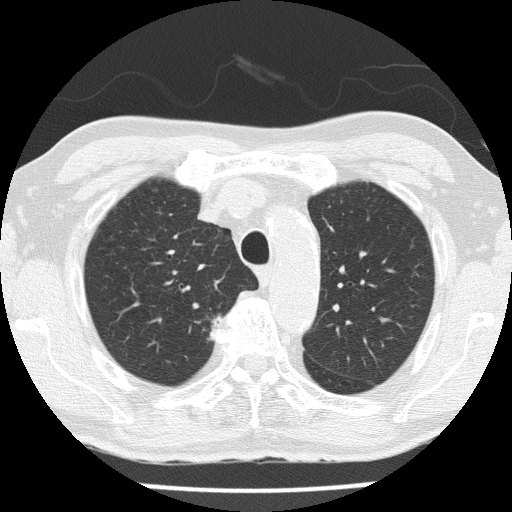
Low-dose screening chest CT, one axial slice. Slice 114 of 153 in the series (ordered by position). Reconstruction kernel FC51. 120 kVp. Lung window (W 1500 / L -600 HU). 512 × 512 image matrix, field of view 323 × 323 mm.
Structures marked on this image (expert manual segmentation):
- lesion 1 (tumor, upper lobe of right lung): bounding box [x1, y1, x2, y2] px = [210, 316, 221, 342]